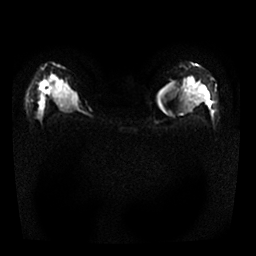
Breast MRI, one axial slice. Slice 15 of 25 in the series (ordered by position). Diffusion-weighted series; image 2 of 4 stored at this slice position (different b-values; order by instance number). 1.5 T. 4 mm slice thickness. 256 × 256 image matrix, field of view 320 × 320 mm. Female patient.
Outlined on this slice (manually delineated by an expert):
- tumour on diffusion-weighted imaging: bounding box <39,81,50,93> (left, top, right, bottom; pixels)